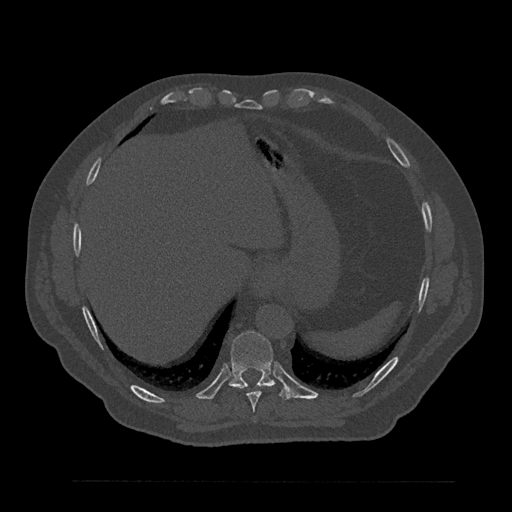
CT including the spine, one axial slice; slice 375 of 797 in the series (ordered by position); 120 kVp; bone window (W 1800 / L 400 HU); 0.5 mm slice thickness; 512 × 512 image matrix, field of view 430 × 430 mm. Patient: male, 61 years. Case-level facts recorded for this patient, not image findings: primary cancer: prostate.
Annotated regions visible in this slice (semi-automatically segmented with operator editing):
- T10 vertebra: bounding box (x1, y1, x2, y2) in pixels: (229, 331, 288, 400)
- T9 vertebra: (236, 383, 268, 412)